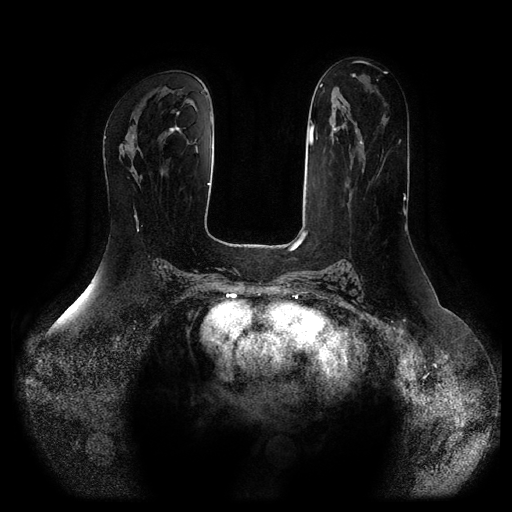
Breast MRI (dynamic contrast-enhanced, multi-phase), one axial slice. Slice 47 of 116 in the series (ordered by position). Dynamic contrast-enhanced series, time point 2 of 5 at this slice position (early post-contrast). 1.5 T. TE 2.5 ms, TR 5.2 ms. 2 mm slice thickness. 512 × 512 image matrix, field of view 400 × 400 mm. Patient: female, 66 years.
Outlined on this slice (semi-automatically segmented with operator editing):
- breast lesion (labelled 'tumour' in the annotation; benign lesions carry a separate 'benign' label): bounding box (x1, y1, x2, y2) in pixels: (169, 125, 182, 134)